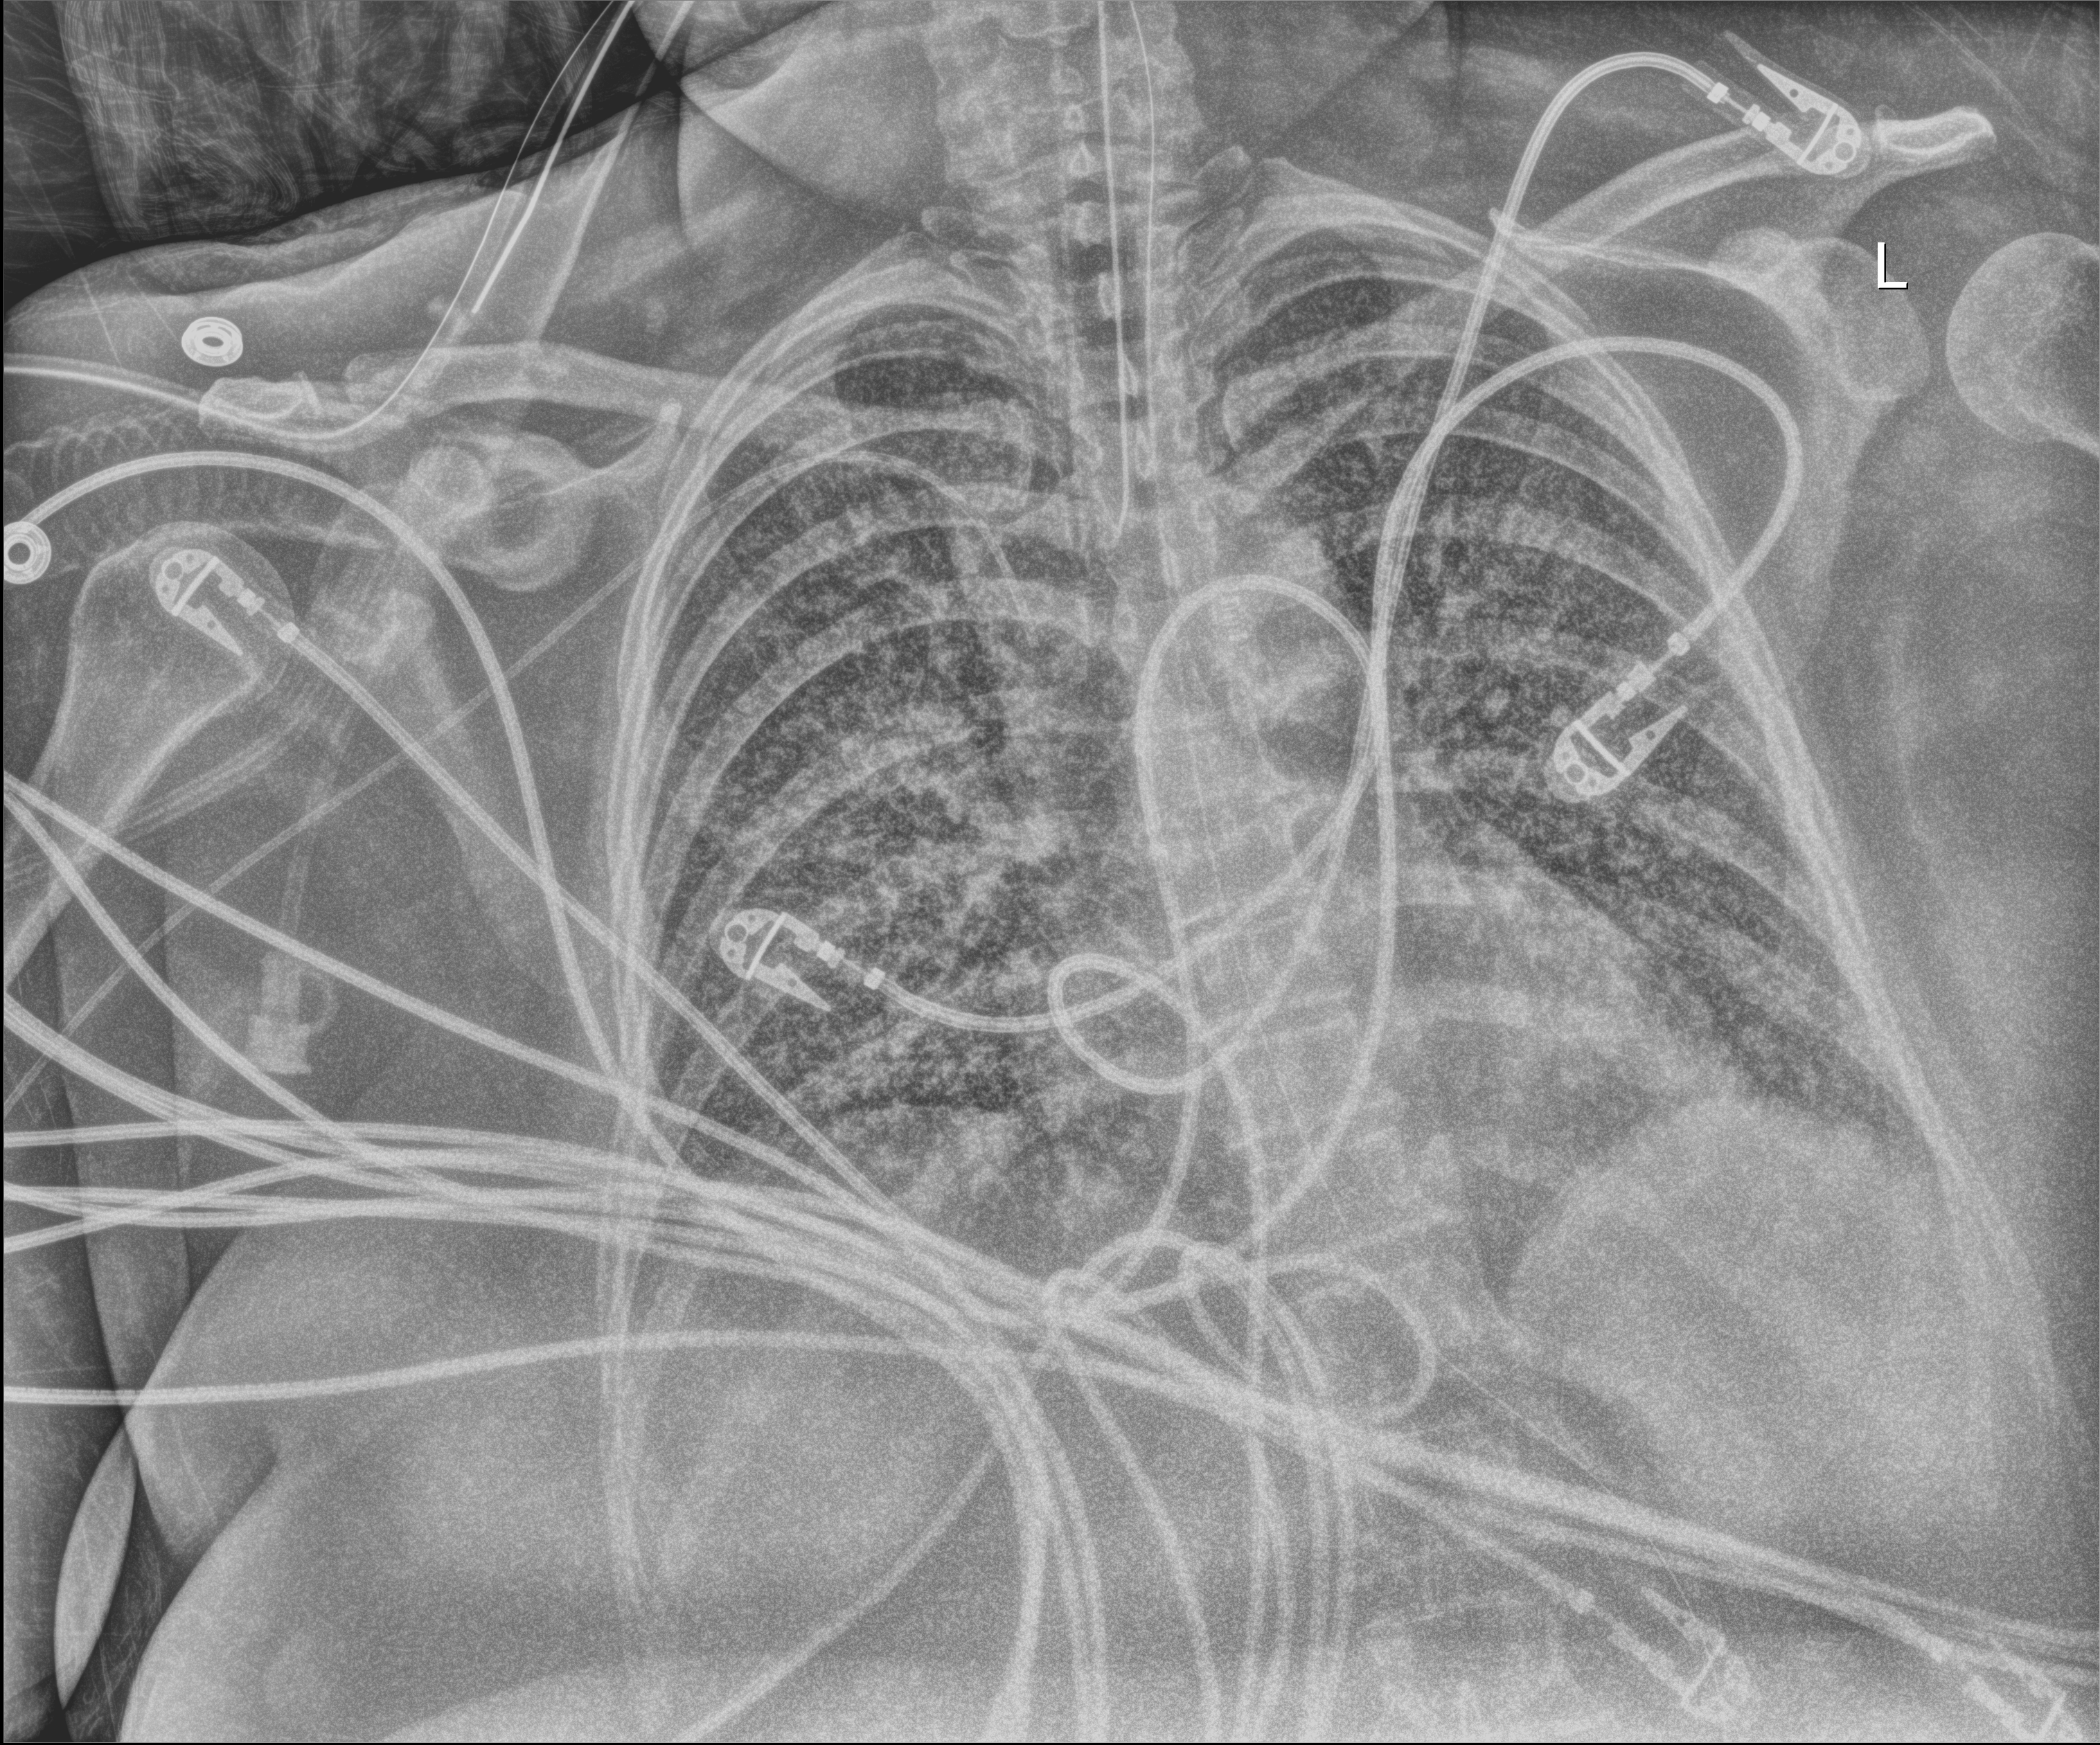
Chest X-ray (portable), anteroposterior (AP) projection. Patient hospitalised with COVID-19; female, aged 18–59 years.
From the hospital-stay record, not from the radiograph (when in the stay this image was taken is not recorded): admitted to intensive care during this hospital stay: yes.